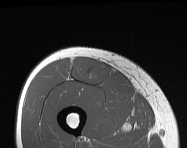
MRI of an extremity soft-tissue mass, one axial slice. Position 56 of 114 along the scan axis. MR volume resampled by the dataset authors to the PET/CT grid (not the native acquisition matrix). 3.27 mm slice thickness. 187 × 148 image matrix, field of view 183 × 145 mm. Male patient. From the clinical record (not read from this slice): histological type: pleiomorphic leiomyosarcoma; grade: intermediate; site of the primary tumour: right thigh.
Annotated regions visible in this slice (expert contour drawn on MRI and transferred to this co-registered scan by the dataset authors):
- gross tumour volume including surrounding oedema: bounding box (x1, y1, x2, y2) in pixels: (72, 56, 110, 85)